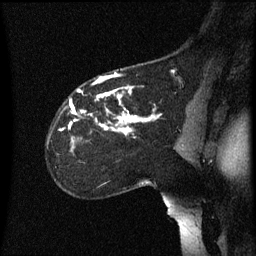
Breast MRI (dynamic contrast-enhanced), one sagittal slice; position 42 of 60 along the scan axis; dynamic contrast-enhanced series, image 2 of 3 at this slice position (ordered by acquisition); 1.5 T; TE 4.2 ms, TR 8.4 ms; 2.2 mm slice thickness; 256 × 256 image matrix, field of view 200 × 200 mm. Patient: female, 35 years. Case-level facts recorded for this patient, not image findings: setting: breast cancer imaged before/during neoadjuvant chemotherapy; receptor status: HER2-positive.
Structures marked on this image (semi-automatic segmentation, software-assisted and operator-edited):
- analysis volume of interest (the breast-tissue region the enhancement analysis was run in; not a lesion): bounding box [x1, y1, x2, y2] px = [47, 72, 178, 169]
- tumour enhancement mask (voxels above the 70 % enhancement threshold inside the analysis volume of interest): [61, 72, 161, 135]